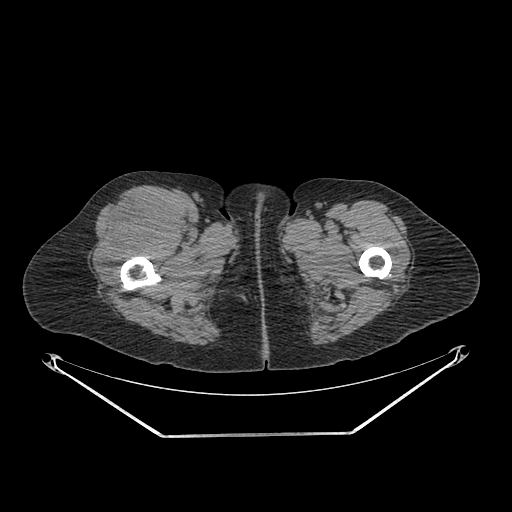
CT of an extremity soft-tissue mass (from a PET/CT study), one axial slice; position 274 of 311 along the scan axis; reconstruction kernel SOFT; 140 kVp; soft-tissue window (W 400 / L 40 HU); 3.75 mm slice thickness; 512 × 512 image matrix, field of view 500 × 500 mm. Female patient. From the clinical record (not read from this slice): histological type: pleiomorphic undifferentiated sarcoma; grade: high; site of the primary tumour: right quadricep.
Annotated regions visible in this slice (expert contour drawn on MRI and transferred to this co-registered scan by the dataset authors):
- tumour plus oedema (research contour): bounding box (x1, y1, x2, y2) in pixels: (96, 194, 175, 271)
- tumour (research contour): (96, 194, 175, 271)